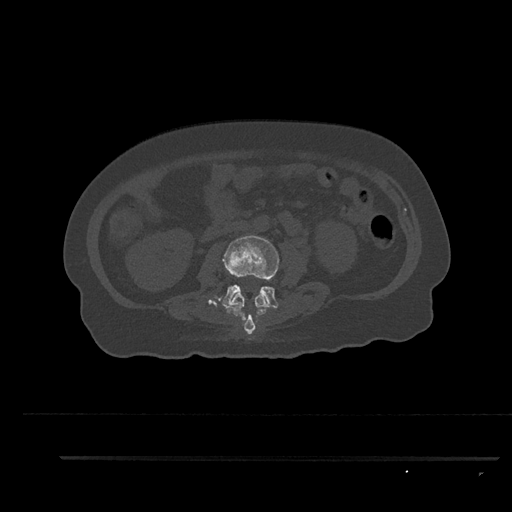
CT including the spine, one axial slice; slice 114 of 797 in the series (ordered by position); reconstruction kernel Br40s/3; bone window (W 1800 / L 400 HU); 0.5 mm slice thickness; 512 × 512 image matrix, field of view 408 × 408 mm. Patient: female, 44 years. From the clinical record (not read from this slice): primary cancer: renal.
Outlined on this slice (semi-automatic segmentation, software-assisted and operator-edited):
- L2 vertebra: bounding box (x1, y1, x2, y2) in pixels: (224, 293, 268, 335)
- L3 vertebra: (219, 235, 280, 309)